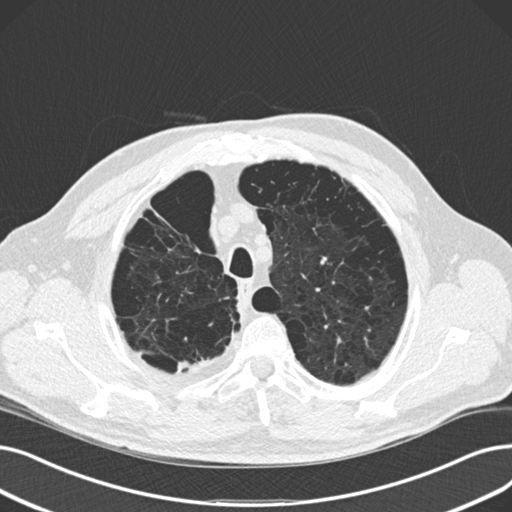
Low-dose screening chest CT, one axial slice. Lung window (W 1500 / L -600 HU). 2 mm slice thickness. 512 × 512 image matrix, field of view 369 × 369 mm.
Outlined on this slice (expert manual segmentation):
- lesion 2 (tumor, upper lobe of right lung): bounding box <178,363,189,369> (left, top, right, bottom; pixels)